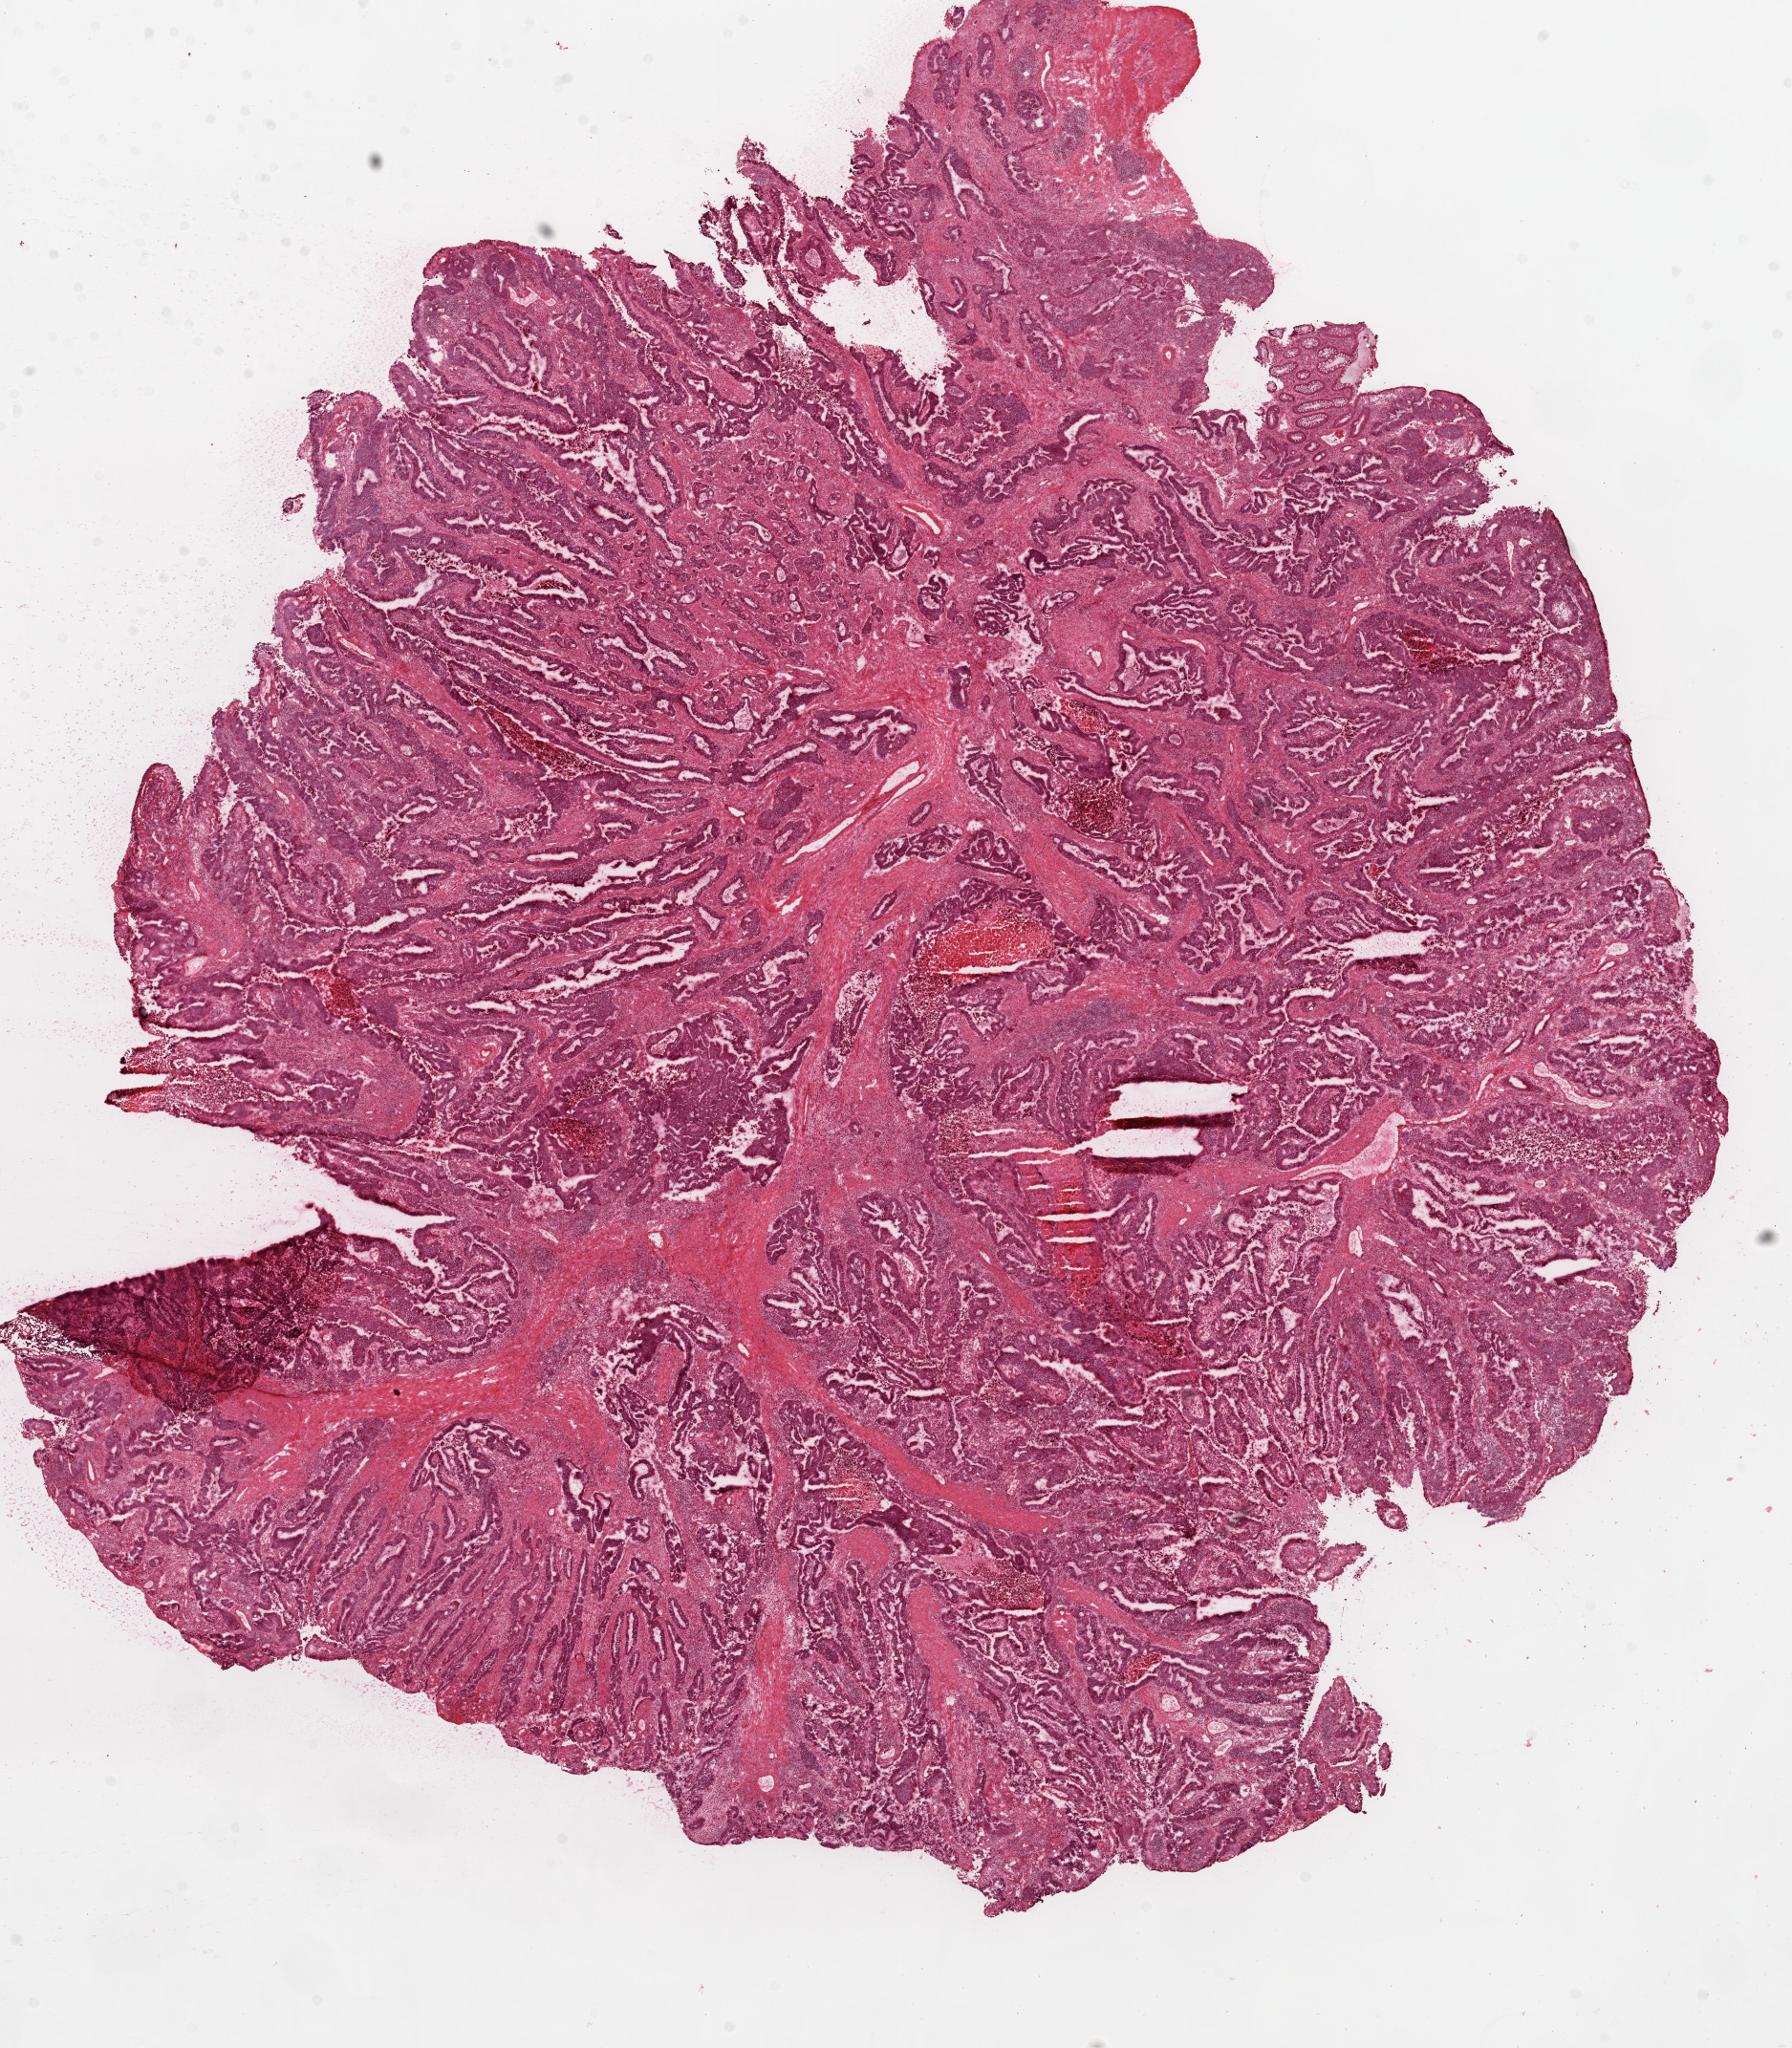
Whole-slide histology image, H&E-stained, a low-resolution overview of the entire scanned area, about 15.0 x 17.2 mm (from a 20x scan), frozen section, colon, primary tumour sample. Patient: female, age at initial diagnosis 34 years.
Pathologic diagnosis: Adenocarcinoma, NOS.